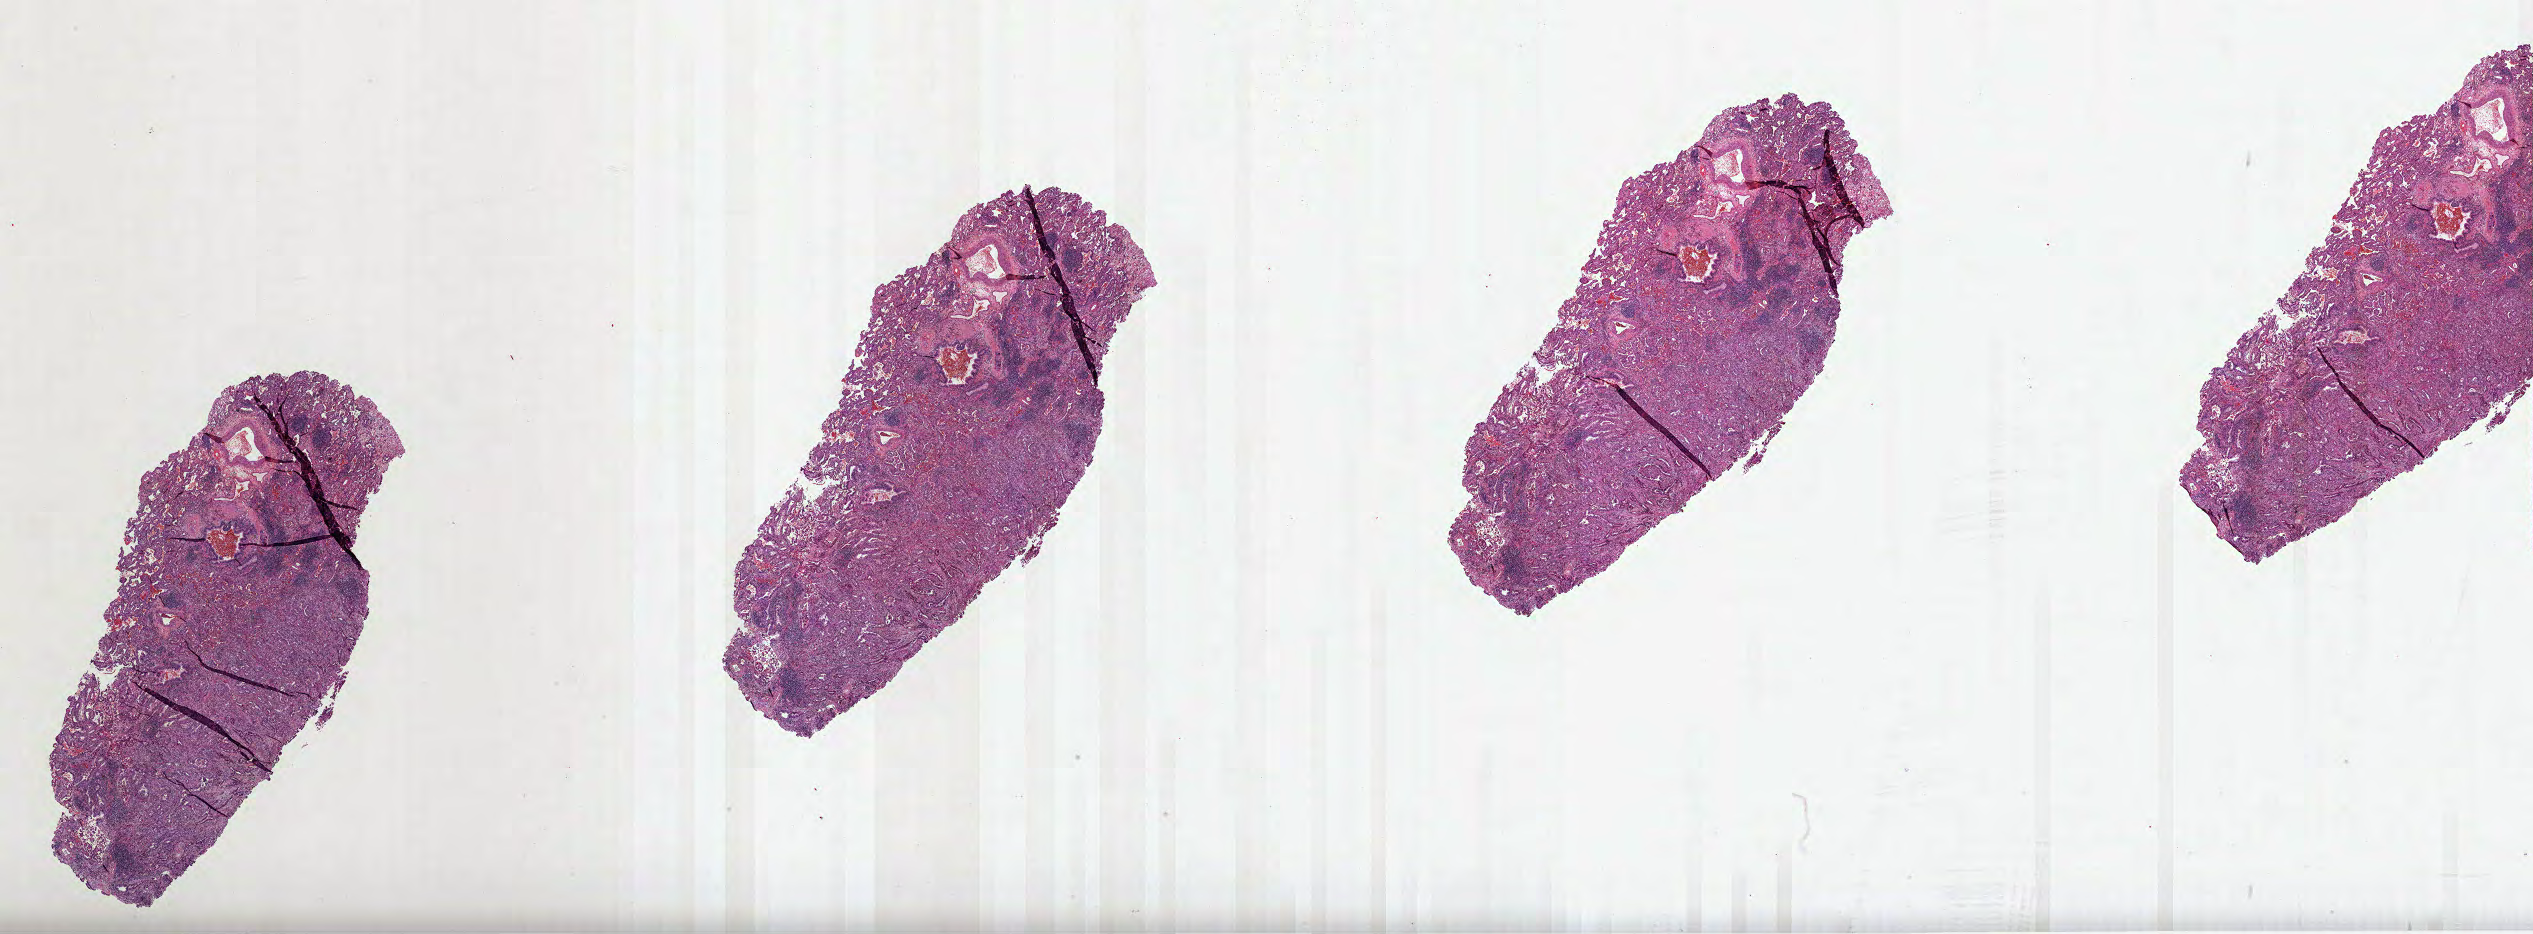
Whole-slide histology image, H&E — whole scanned area (about 40.9 x 15.1 mm, from a 40x scan) shown as a low-resolution overview; FFPE section; primary tumour sample from the lung. Patient: female, age at initial diagnosis 72 years.
AJCC pathologic stage: IB (7th edition). Diagnosis: Adenocarcinoma, NOS (upper lobe, lung). TNM: T2a N0 MX.